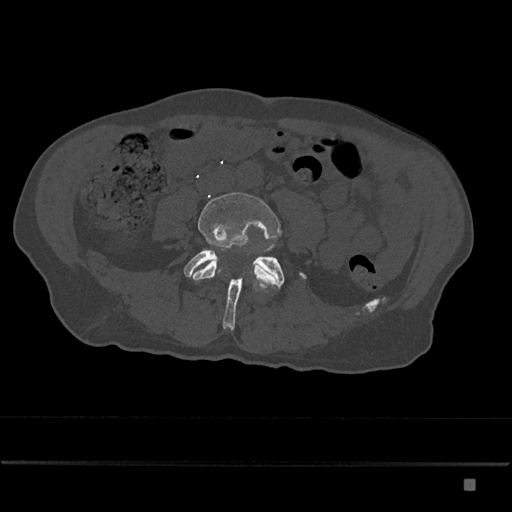
CT including the spine, one axial slice. Position 310 of 797 along the scan axis. 120 kVp. Bone window (W 1800 / L 400 HU). 0.5 mm slice thickness. 512 × 512 image matrix, field of view 390 × 390 mm. Patient: male, 72 years. Case-level facts recorded for this patient, not image findings: primary cancer: prostate.
Structures marked on this image (semi-automatic segmentation, software-assisted and operator-edited):
- L4 vertebra: bounding box [x1, y1, x2, y2] px = [190, 192, 281, 286]
- L5 vertebra: [184, 249, 306, 330]